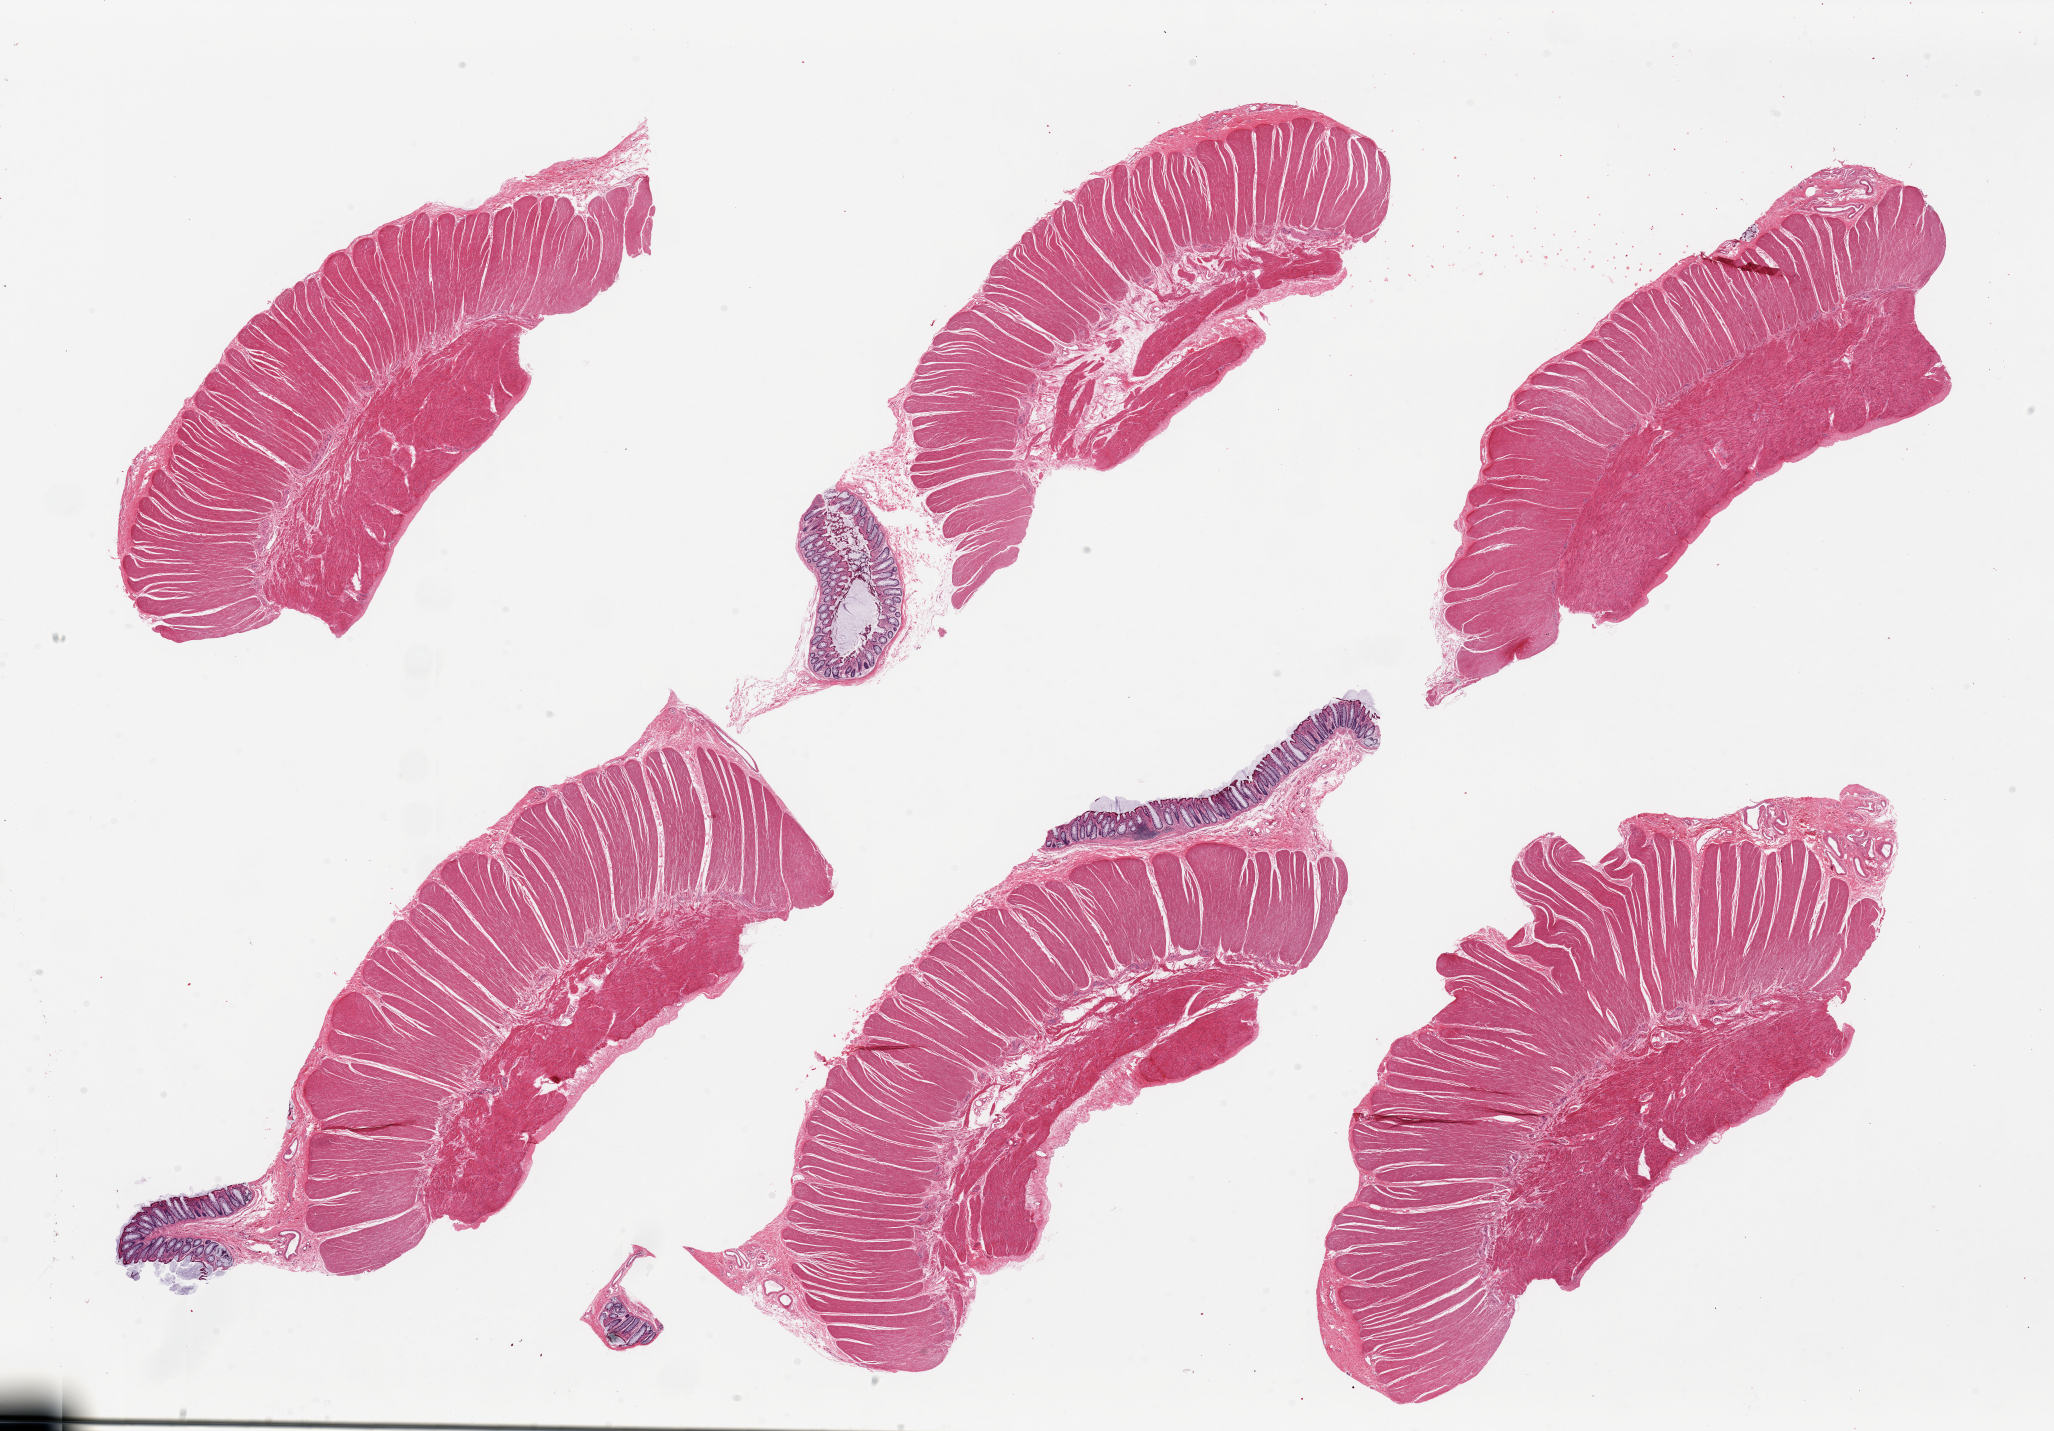
Whole-slide image, haematoxylin and eosin stain — shown as a low-resolution overview of the whole scanned area (about 32.5 x 22.6 mm, acquisition: 20x scan); PAXgene-fixed paraffin-embedded (PFPE) section; sampled site (target tissue): sigmoid colon; tissue donor sample. Donor: male.
Reviewer comment on this tissue sample: 6 pieces; all with full thickness muscle.